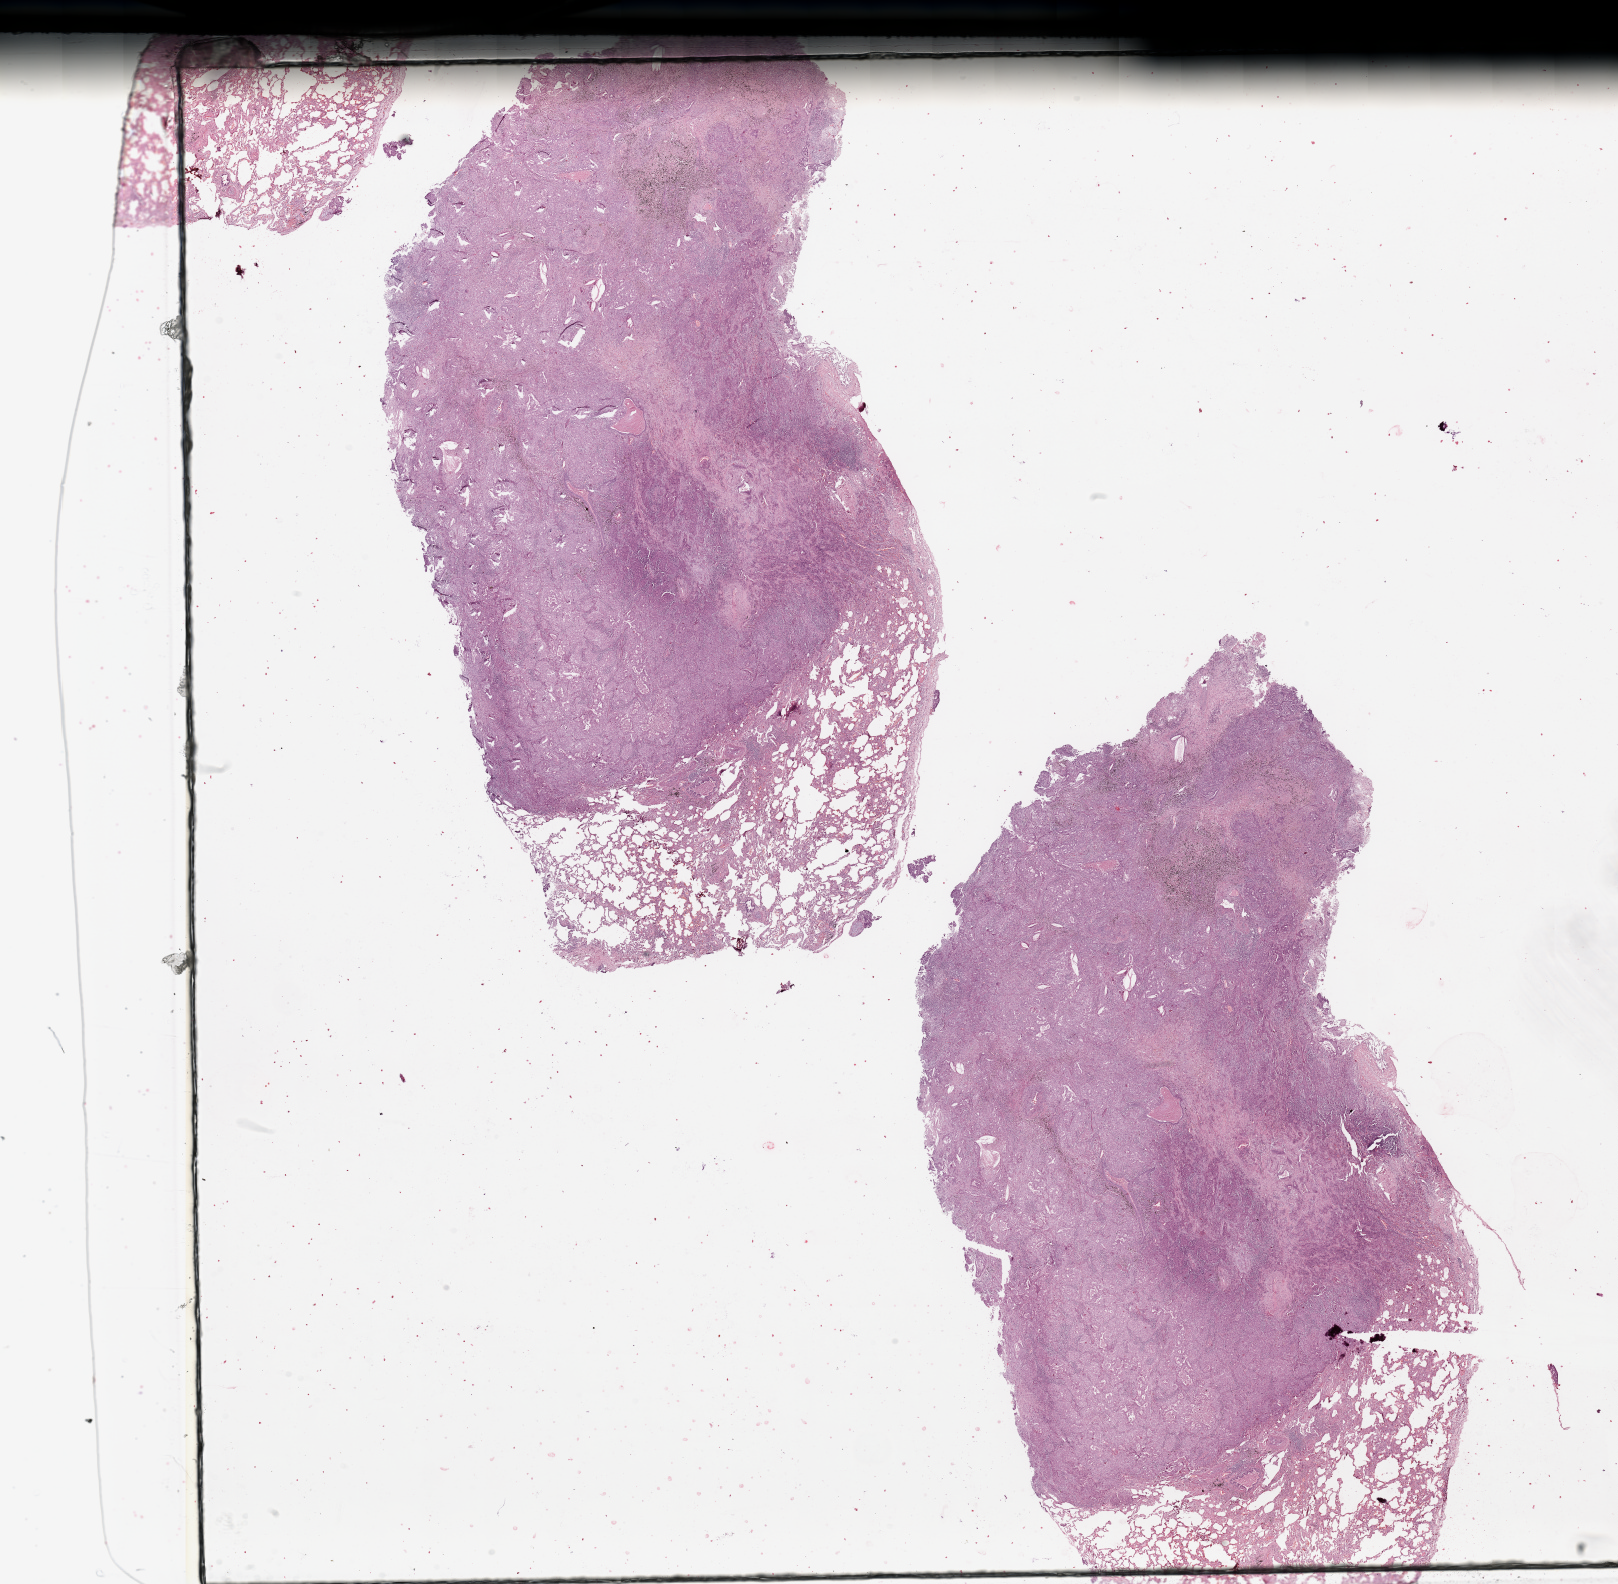
Whole-slide histology image, Hematoxylin and eosin (H&E) stained — whole scanned area (about 25.6 x 25.1 mm, slide scanned at 20x) shown as a low-resolution overview; tumour tissue sample, lung. Patient: male, age 54 years. Histologic grade: G2 (moderately differentiated).
AJCC pathologic stage: IB. Primary tumour site (as recorded): left lower lobe. Diagnosis: Adenocarcinoma, NOS.